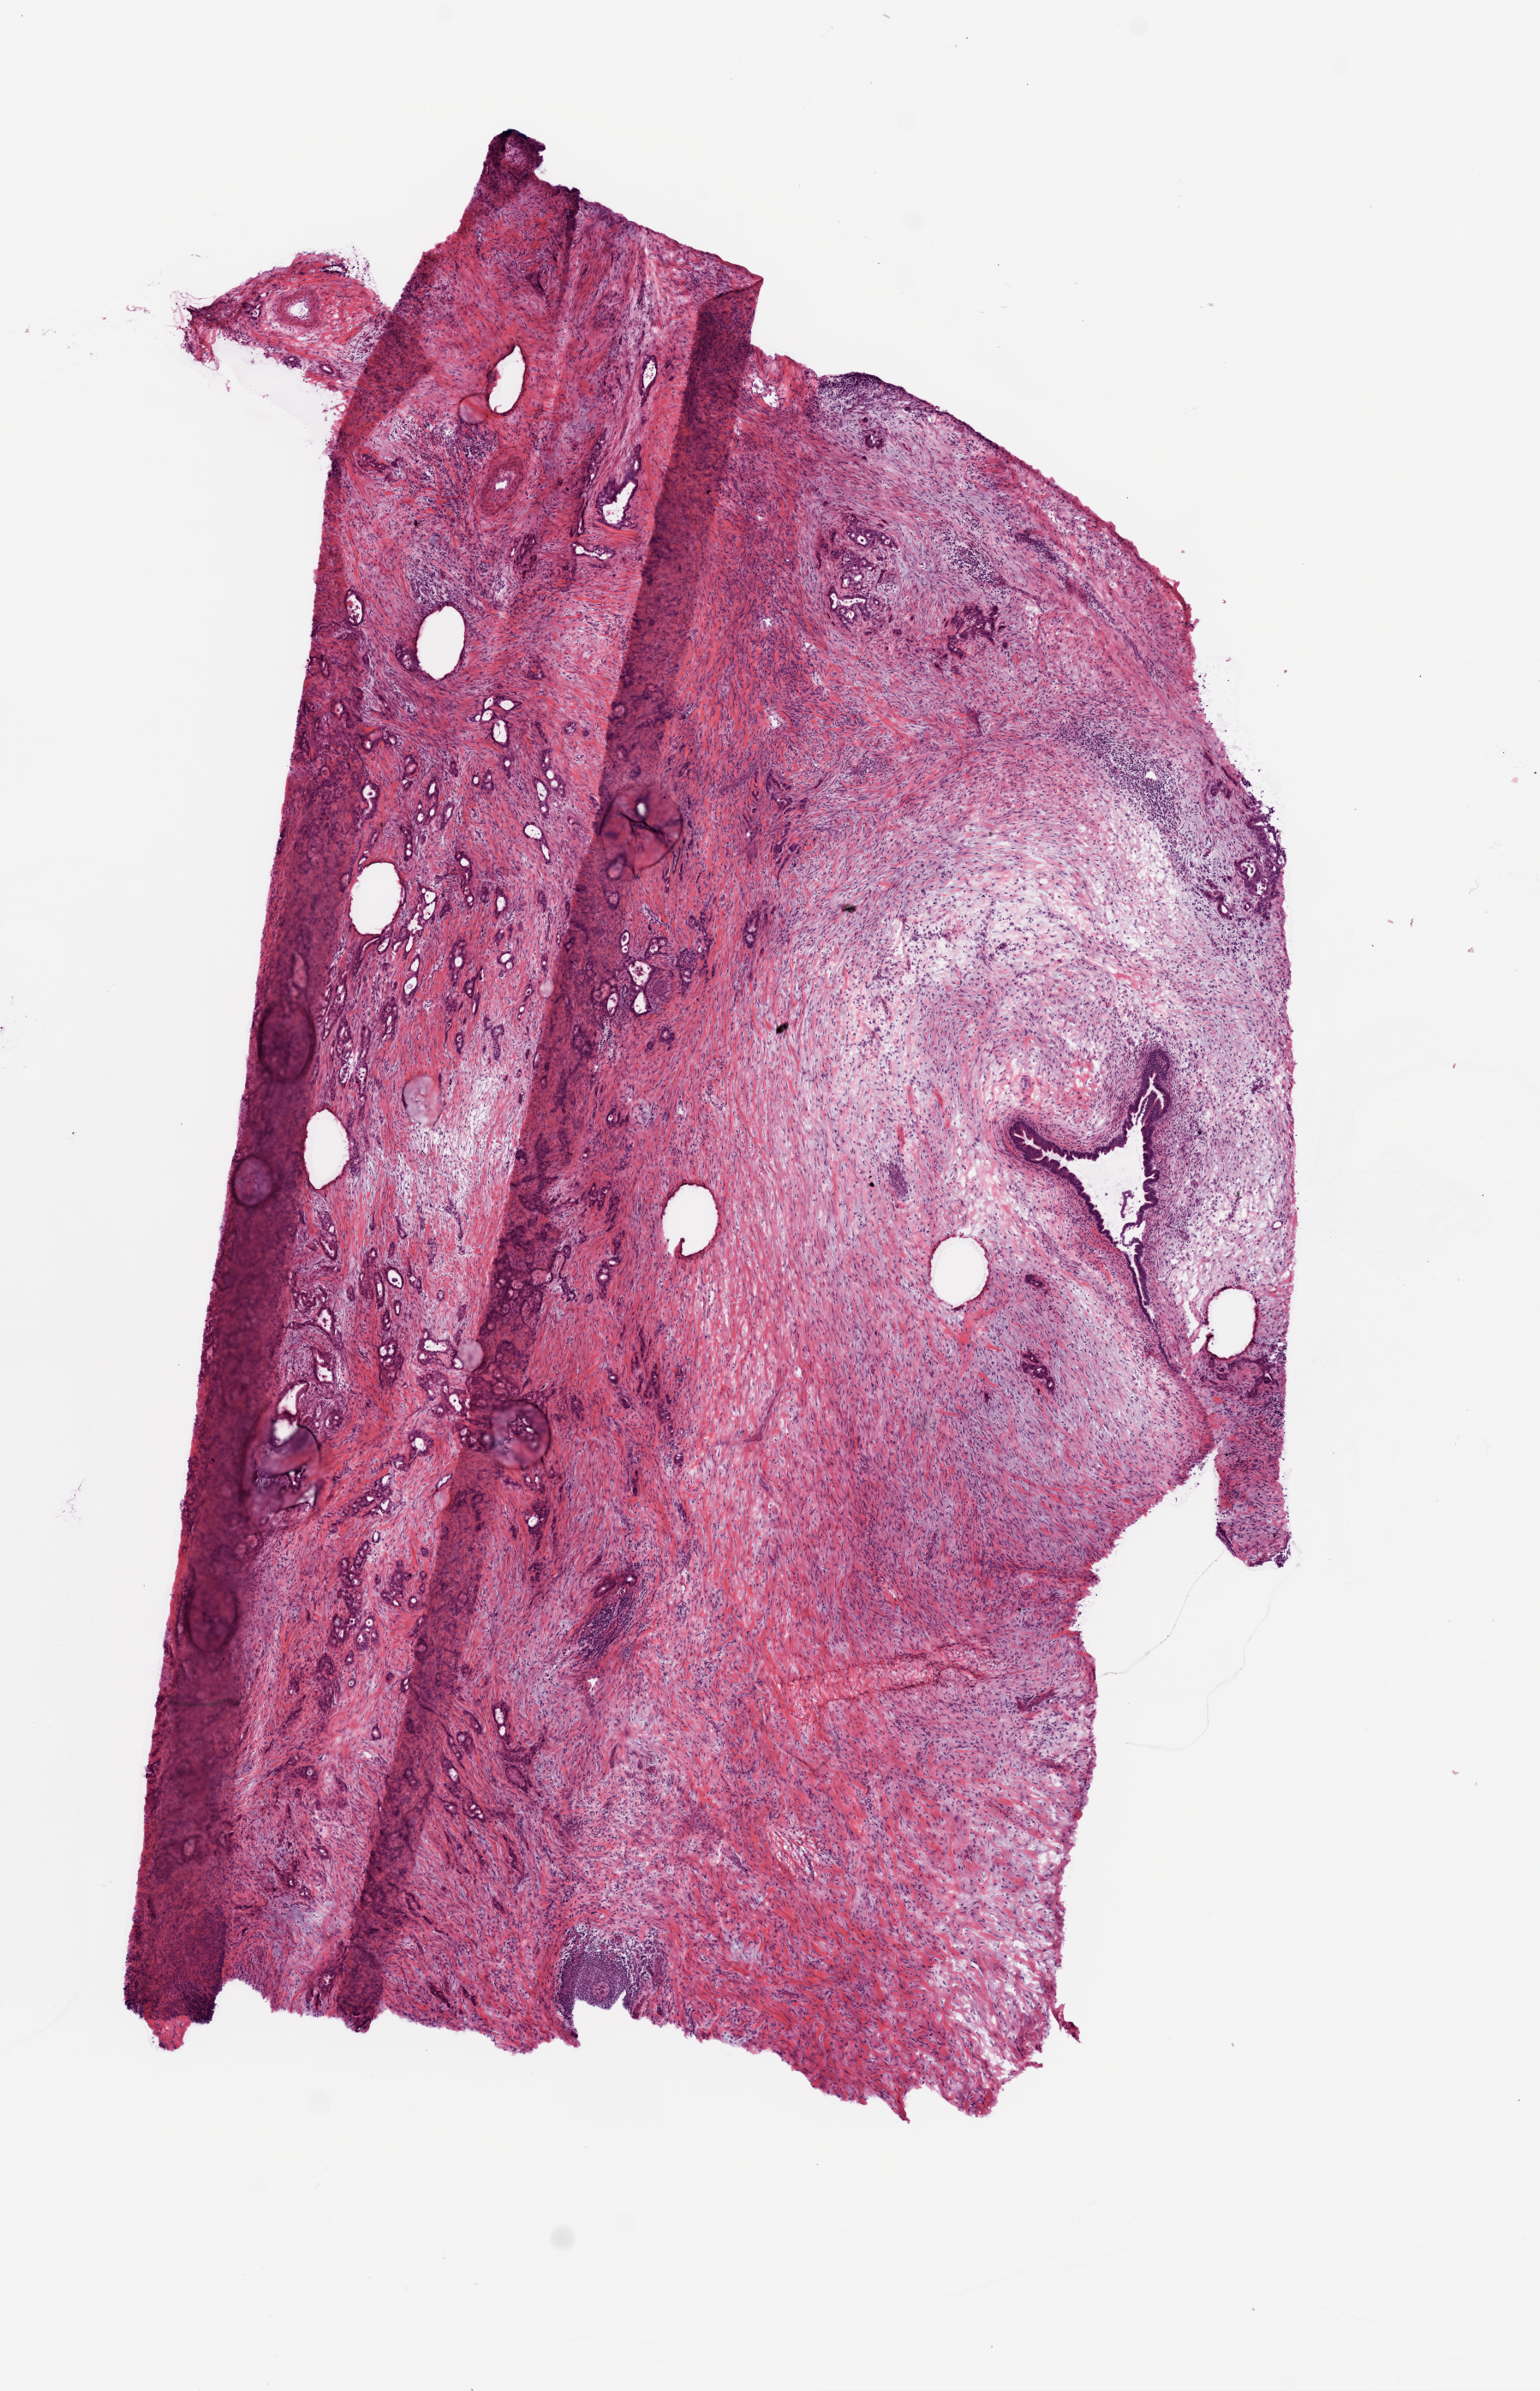
Digitized H&E-stained tissue section (whole slide), shown as a low-resolution overview of the whole scanned area (about 7.3 x 11.3 mm). Frozen section from the top of the tissue portion. Sample: primary tumour, pancreas. Female, age 61 years at initial diagnosis. Composition of this section per pathologist review: tumour nuclei 15%, necrosis 1%.
Pathologic diagnosis: Infiltrating duct carcinoma, NOS (head of pancreas).